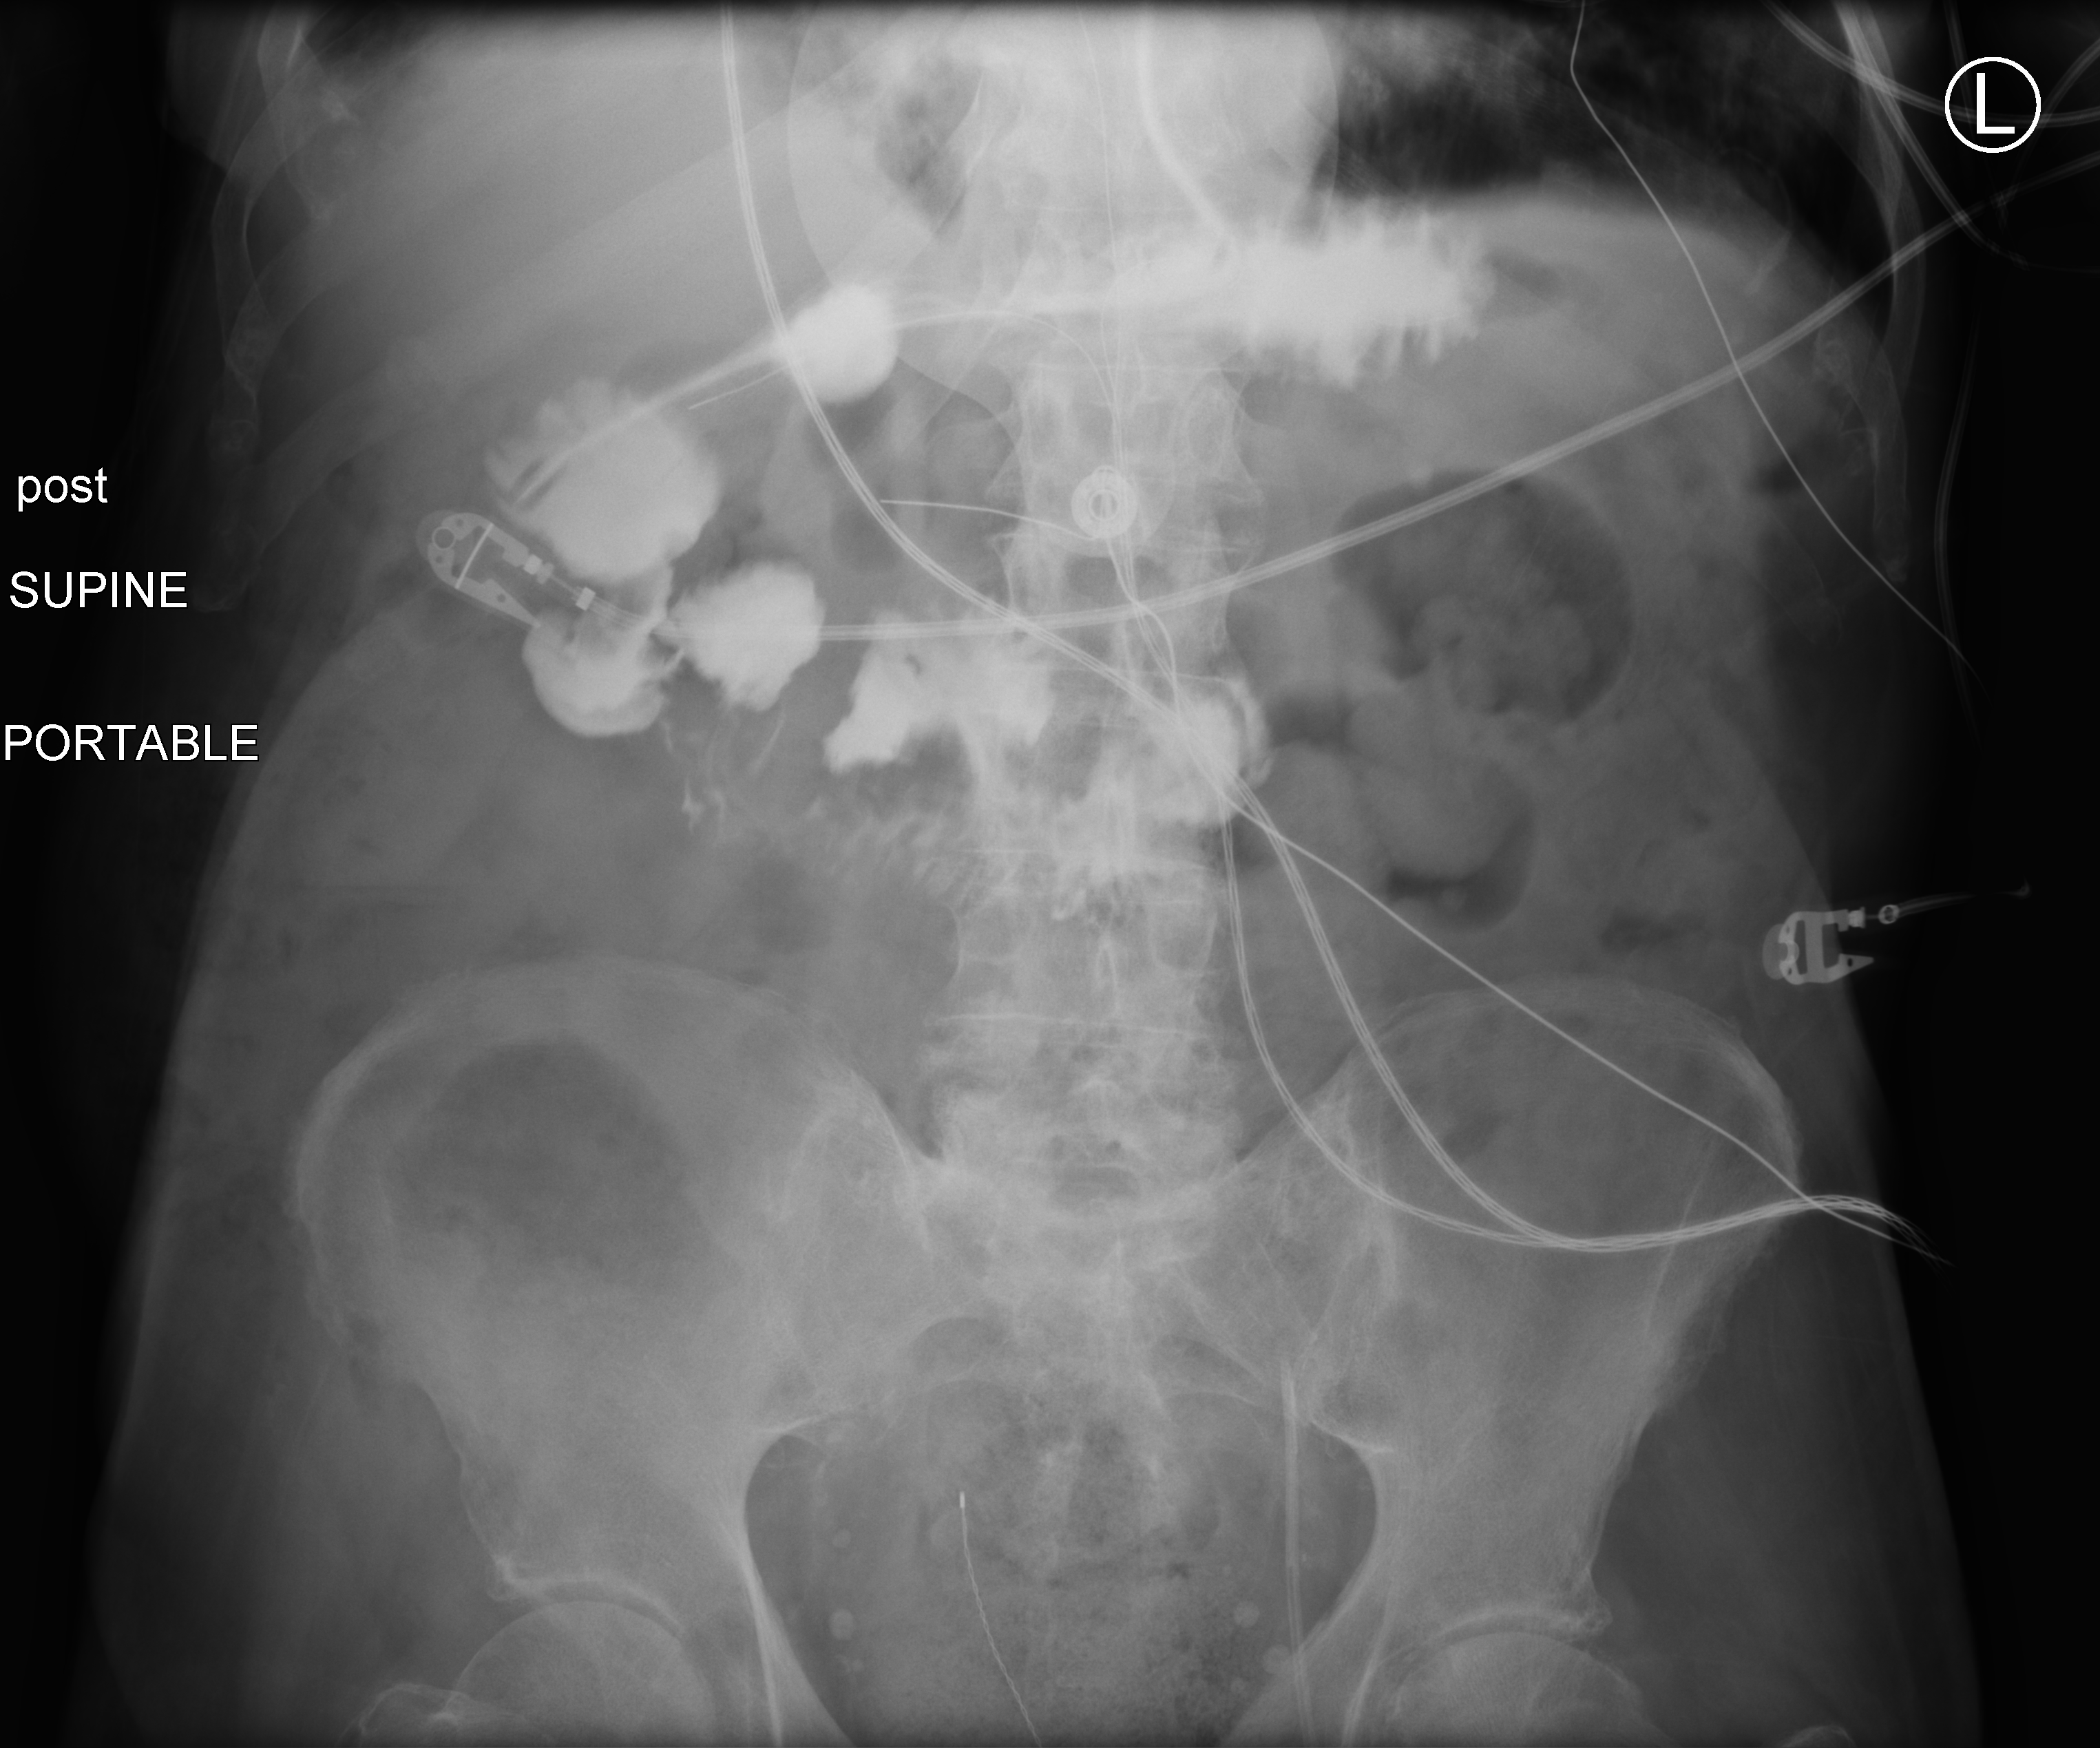
Abdomen X-ray (portable); anteroposterior (AP) projection. Patient hospitalised with COVID-19; male, aged 75–90 years.
Admission-level facts for this patient (not findings on this image; timing relative to this image not recorded): smoking status (admission record): never; admitted to intensive care during this hospital stay: yes; mechanically ventilated during this hospital stay: yes.